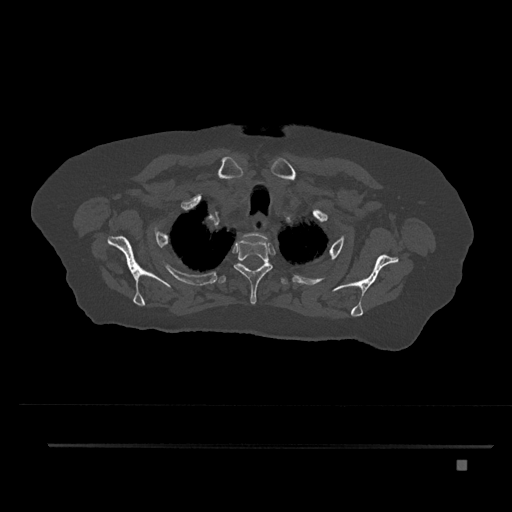
CT including the spine, one axial slice; position 666 of 797 along the scan axis; bone window (W 1800 / L 400 HU); 512 × 512 image matrix, field of view 437 × 437 mm. Patient: female, 76 years. Case-level facts recorded for this patient, not image findings: primary cancer: lung.
Annotated regions visible in this slice (semi-automatic segmentation, software-assisted and operator-edited):
- T1 vertebra: bounding box <243,232,268,245> (left, top, right, bottom; pixels)
- T2 vertebra: <233,239,273,304>
- T3 vertebra: <220,263,287,284>